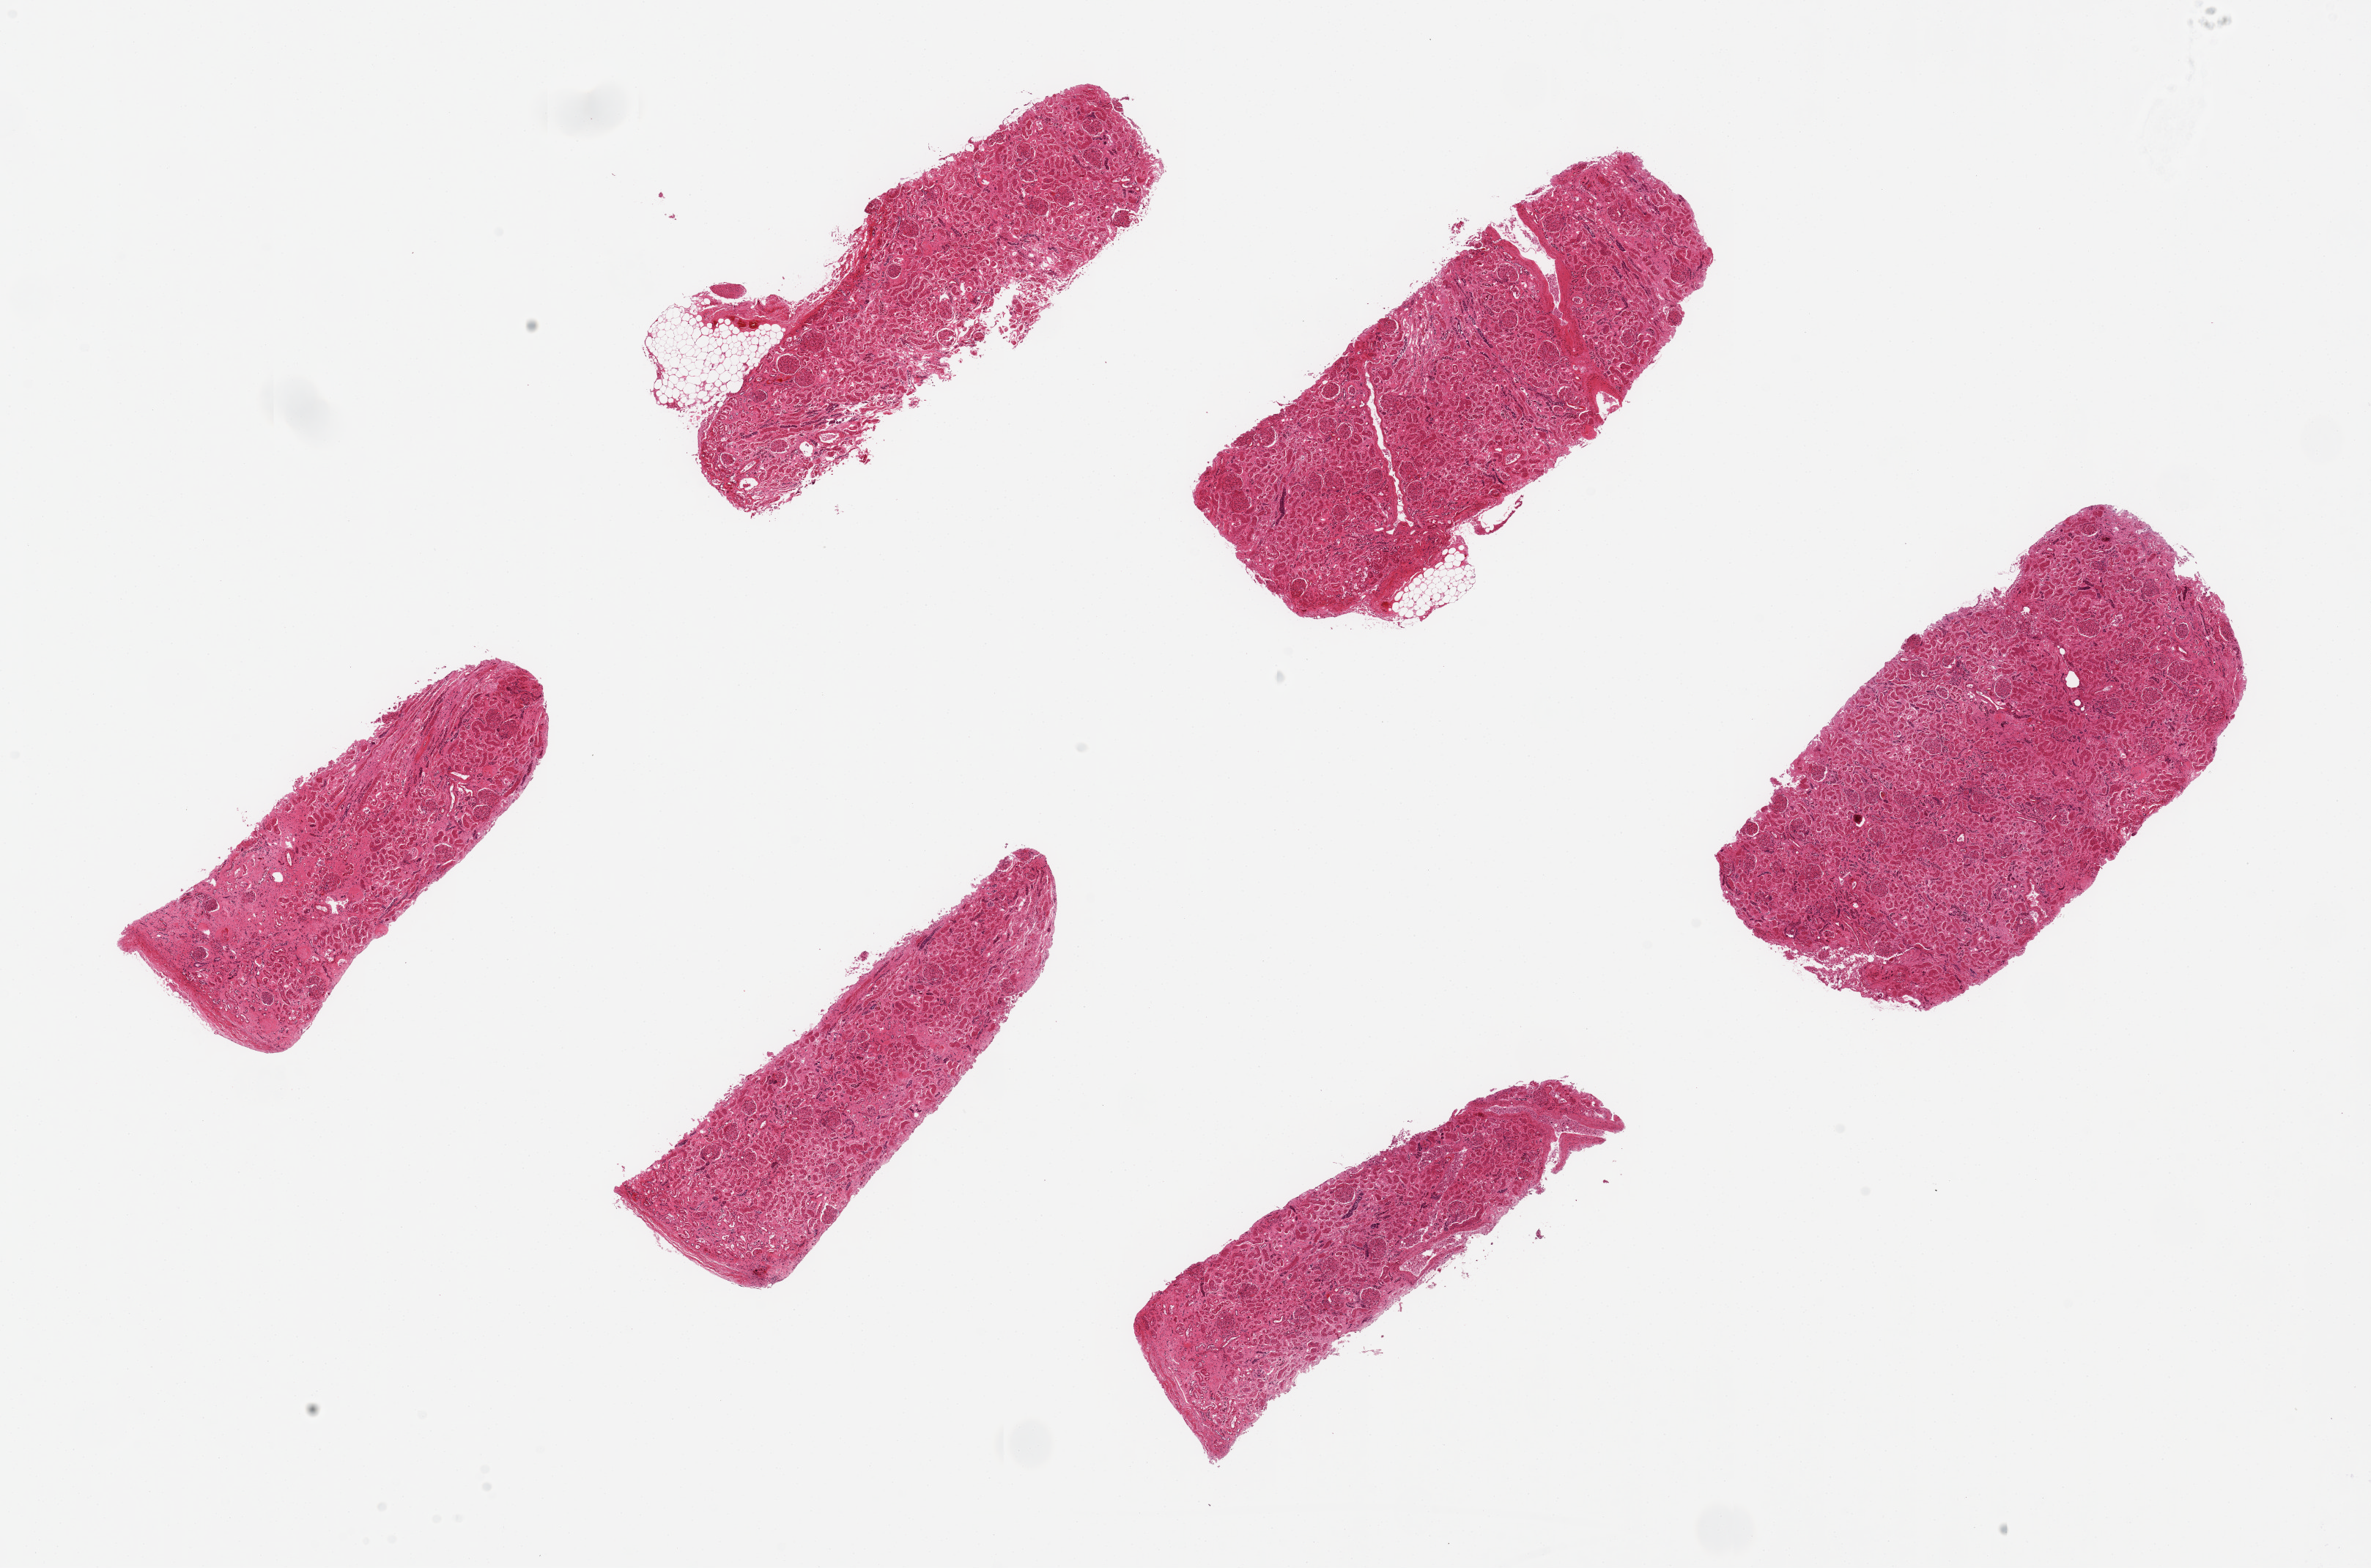
Digitized H&E-stained section, brightfield — low-resolution overview of the scanned area, about 25.6 x 16.9 mm (acquisition: 20x scan), PAXgene-fixed paraffin-embedded (PFPE) section, section of renal cortex (target tissue), donor tissue sample. Donor: male.
Reviewer comment on this tissue sample: 6 pieces, ~6x3mm. Badly autolyzed tubules.